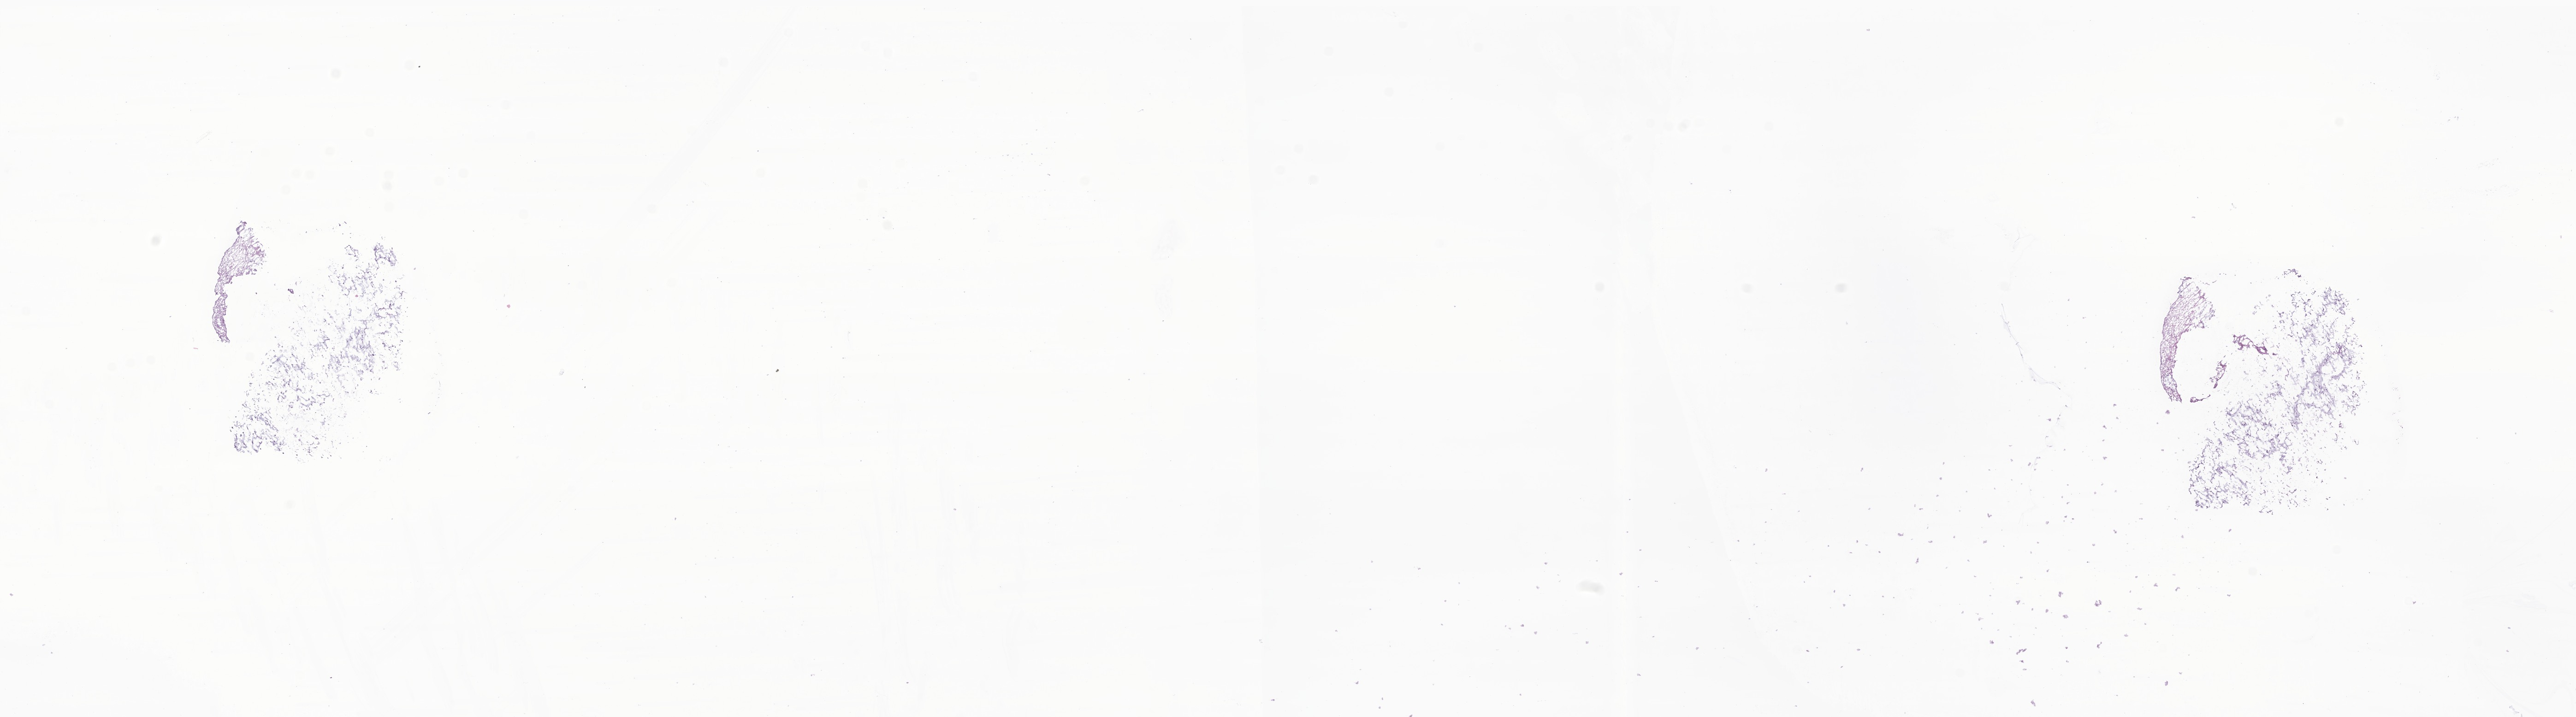
Whole-slide image, haematoxylin and eosin stain of tumor tissue from the brain — a low-resolution overview of the entire scanned area, about 23.6 x 6.6 mm. Frozen section (OCT-embedded). Patient: female, age 136 months (11 years 4 months).
- diagnosis: Atypical teratoid/rhabdoid tumor